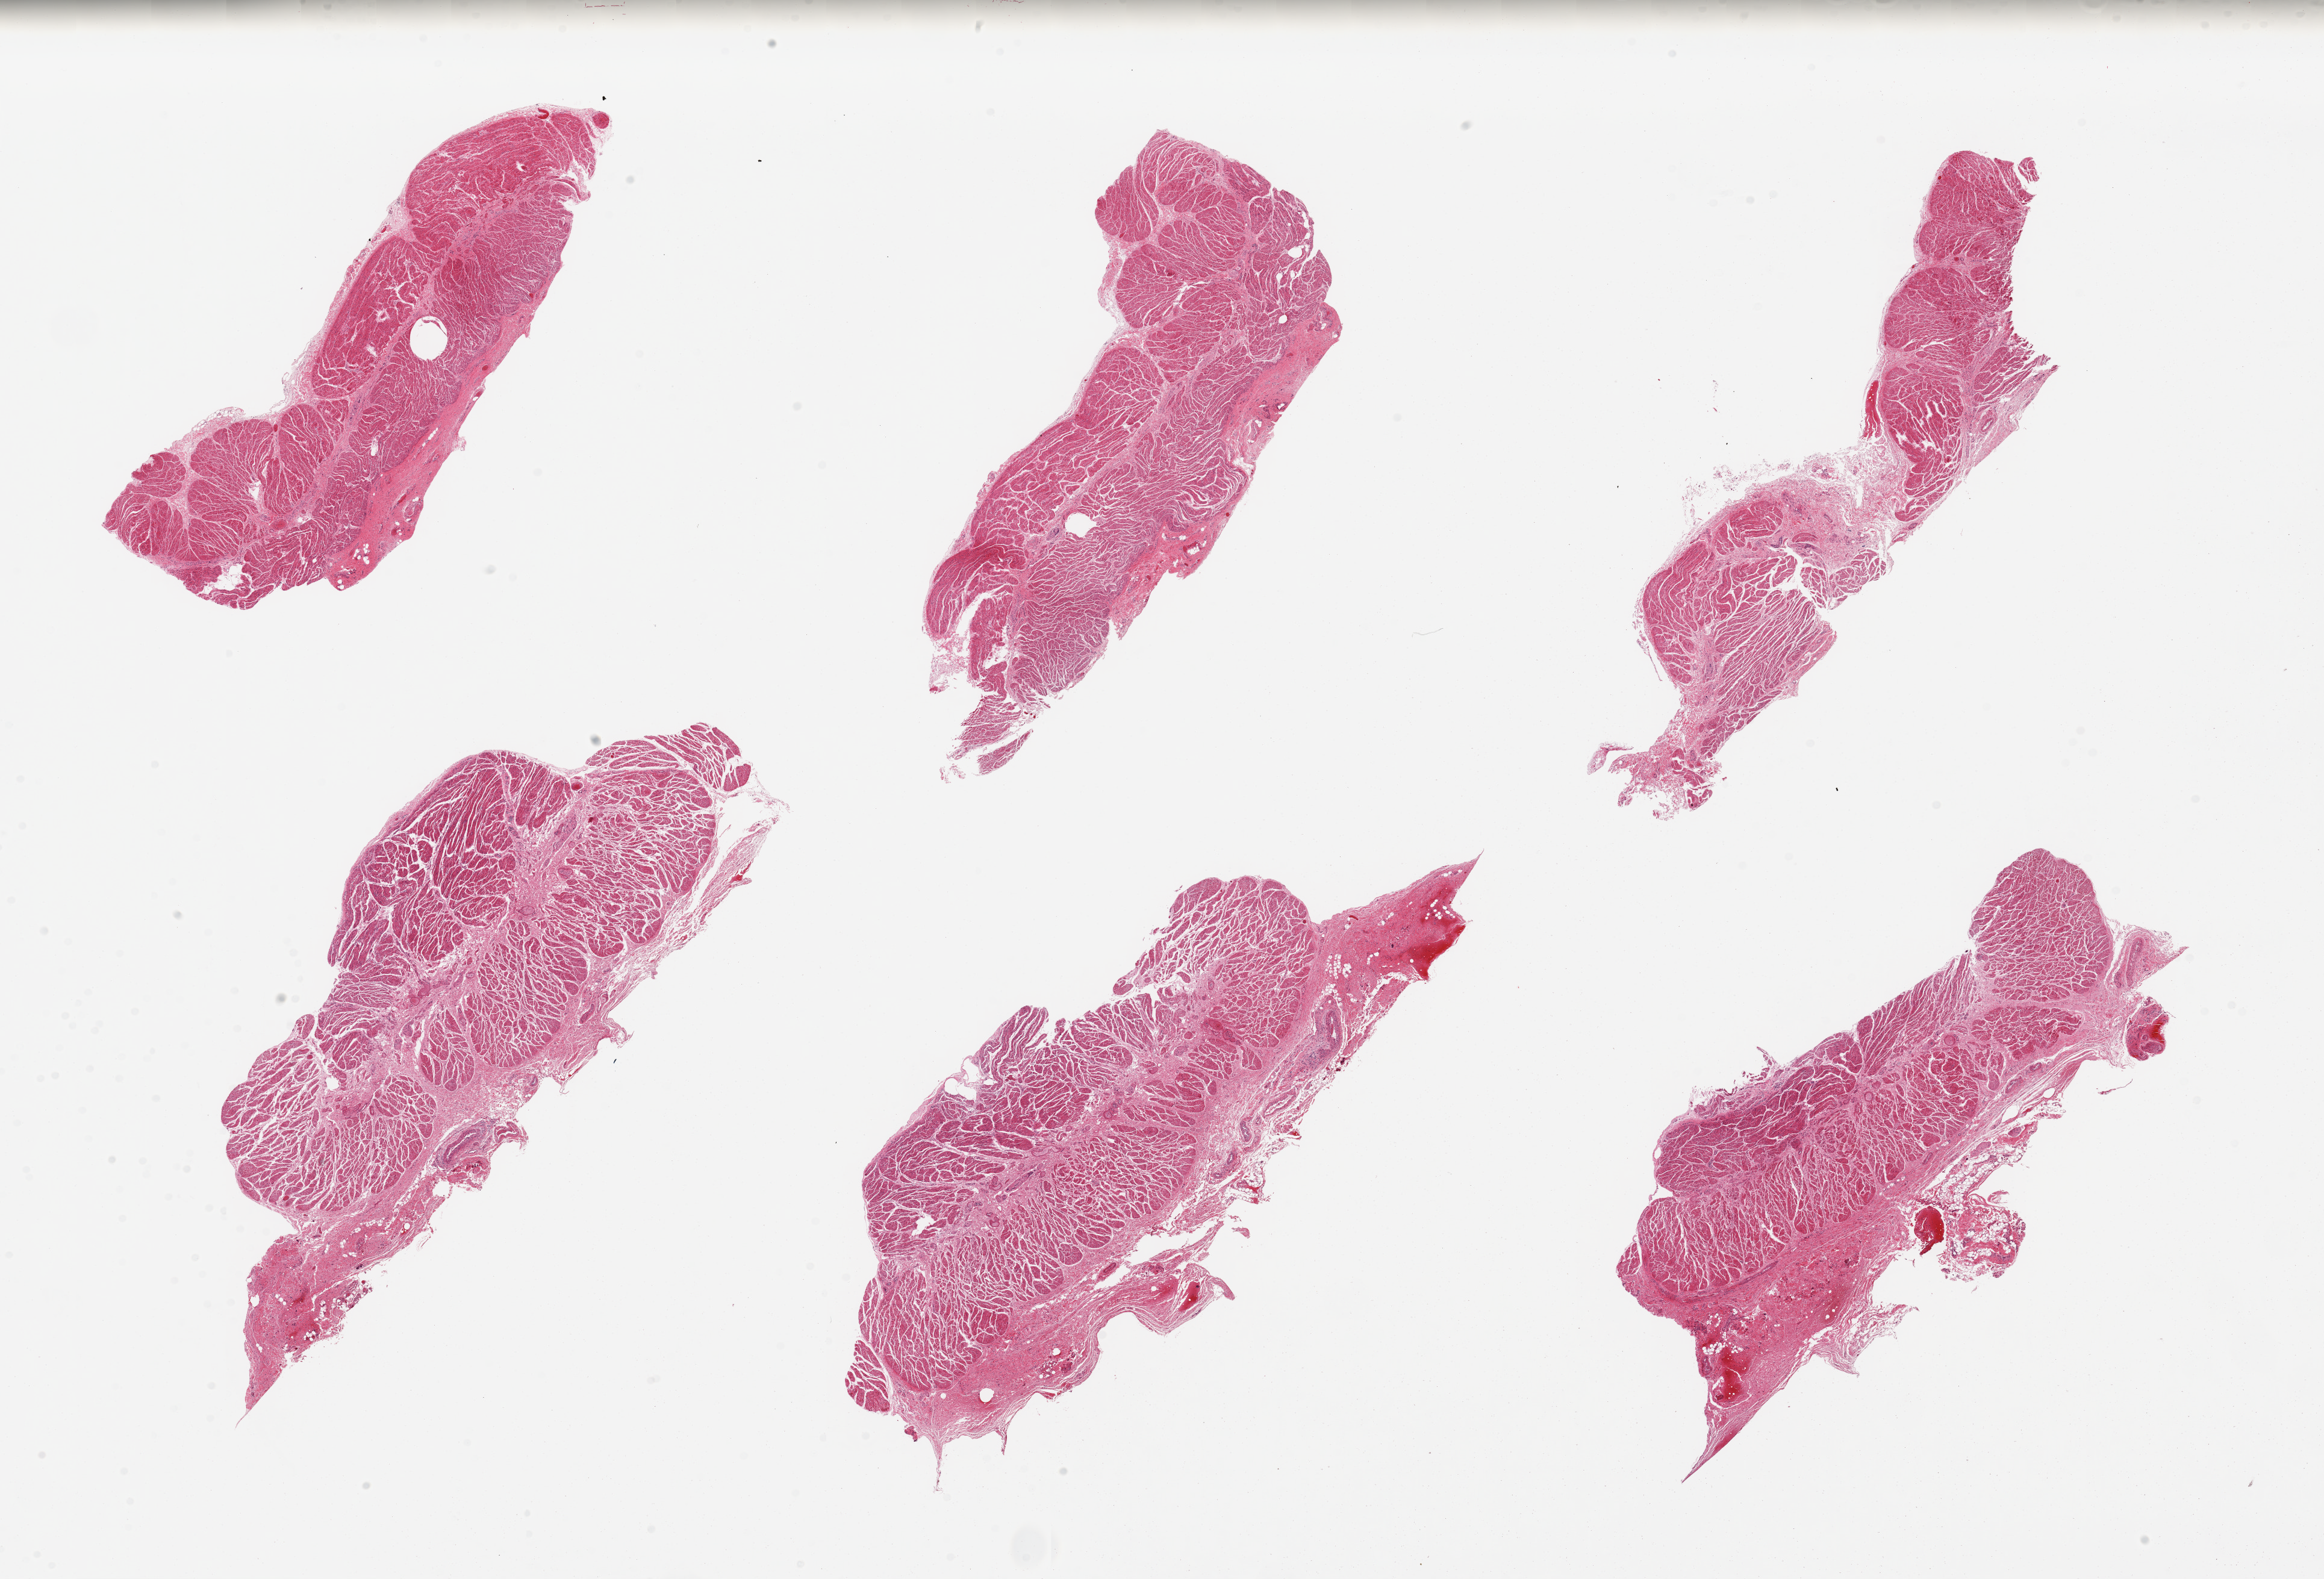
Haematoxylin and eosin whole-slide image, shown as a low-resolution overview of the whole scanned area (about 30.5 x 20.7 mm). PAXgene-fixed, paraffin-embedded tissue. Sampled site (target tissue): gastroesophageal junction. Tissue donor sample. Donor sex: female.
Pathologist's review note for this sample: 6 pieces, all muscularis, good specimens.